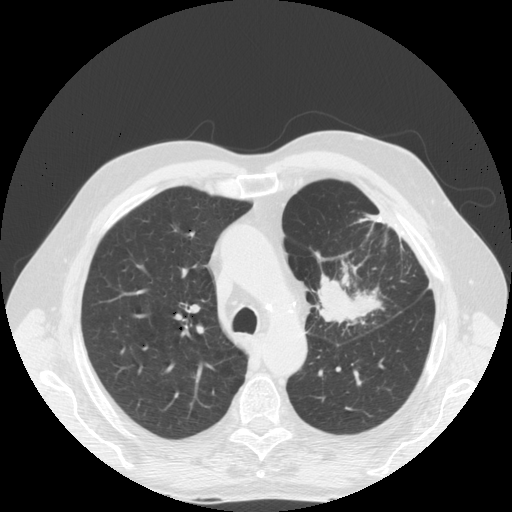
Low-dose screening chest CT, one axial slice. Position 121 of 170 along the scan axis. Reconstruction kernel STANDARD. Lung window (W 1500 / L -600 HU). 512 × 512 image matrix, field of view 380 × 380 mm.
Annotated regions visible in this slice (expert manual segmentation):
- lesion 1 (tumor, upper lobe of left lung): bounding box (x1, y1, x2, y2) in pixels: (315, 275, 383, 326)